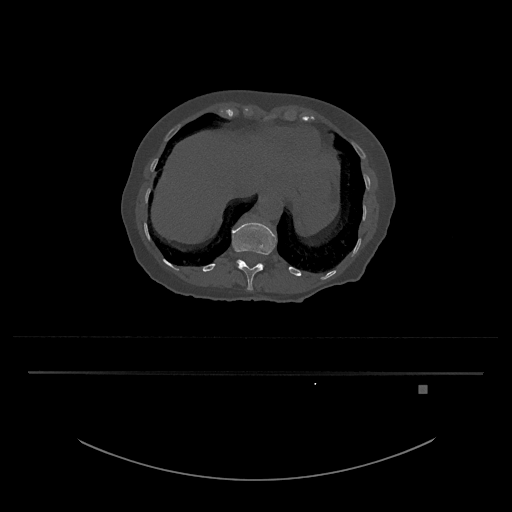
CT including the spine, one axial slice; position 602 of 797 along the scan axis; reconstruction kernel Br40s/3; bone window (W 1800 / L 400 HU); 512 × 512 image matrix, field of view 500 × 500 mm. Patient: female, 57 years. From the clinical record (not read from this slice): primary cancer: cervical.
Annotated regions visible in this slice (semi-automatic segmentation, software-assisted and operator-edited):
- T12 vertebra: bounding box <232,222,277,291> (left, top, right, bottom; pixels)